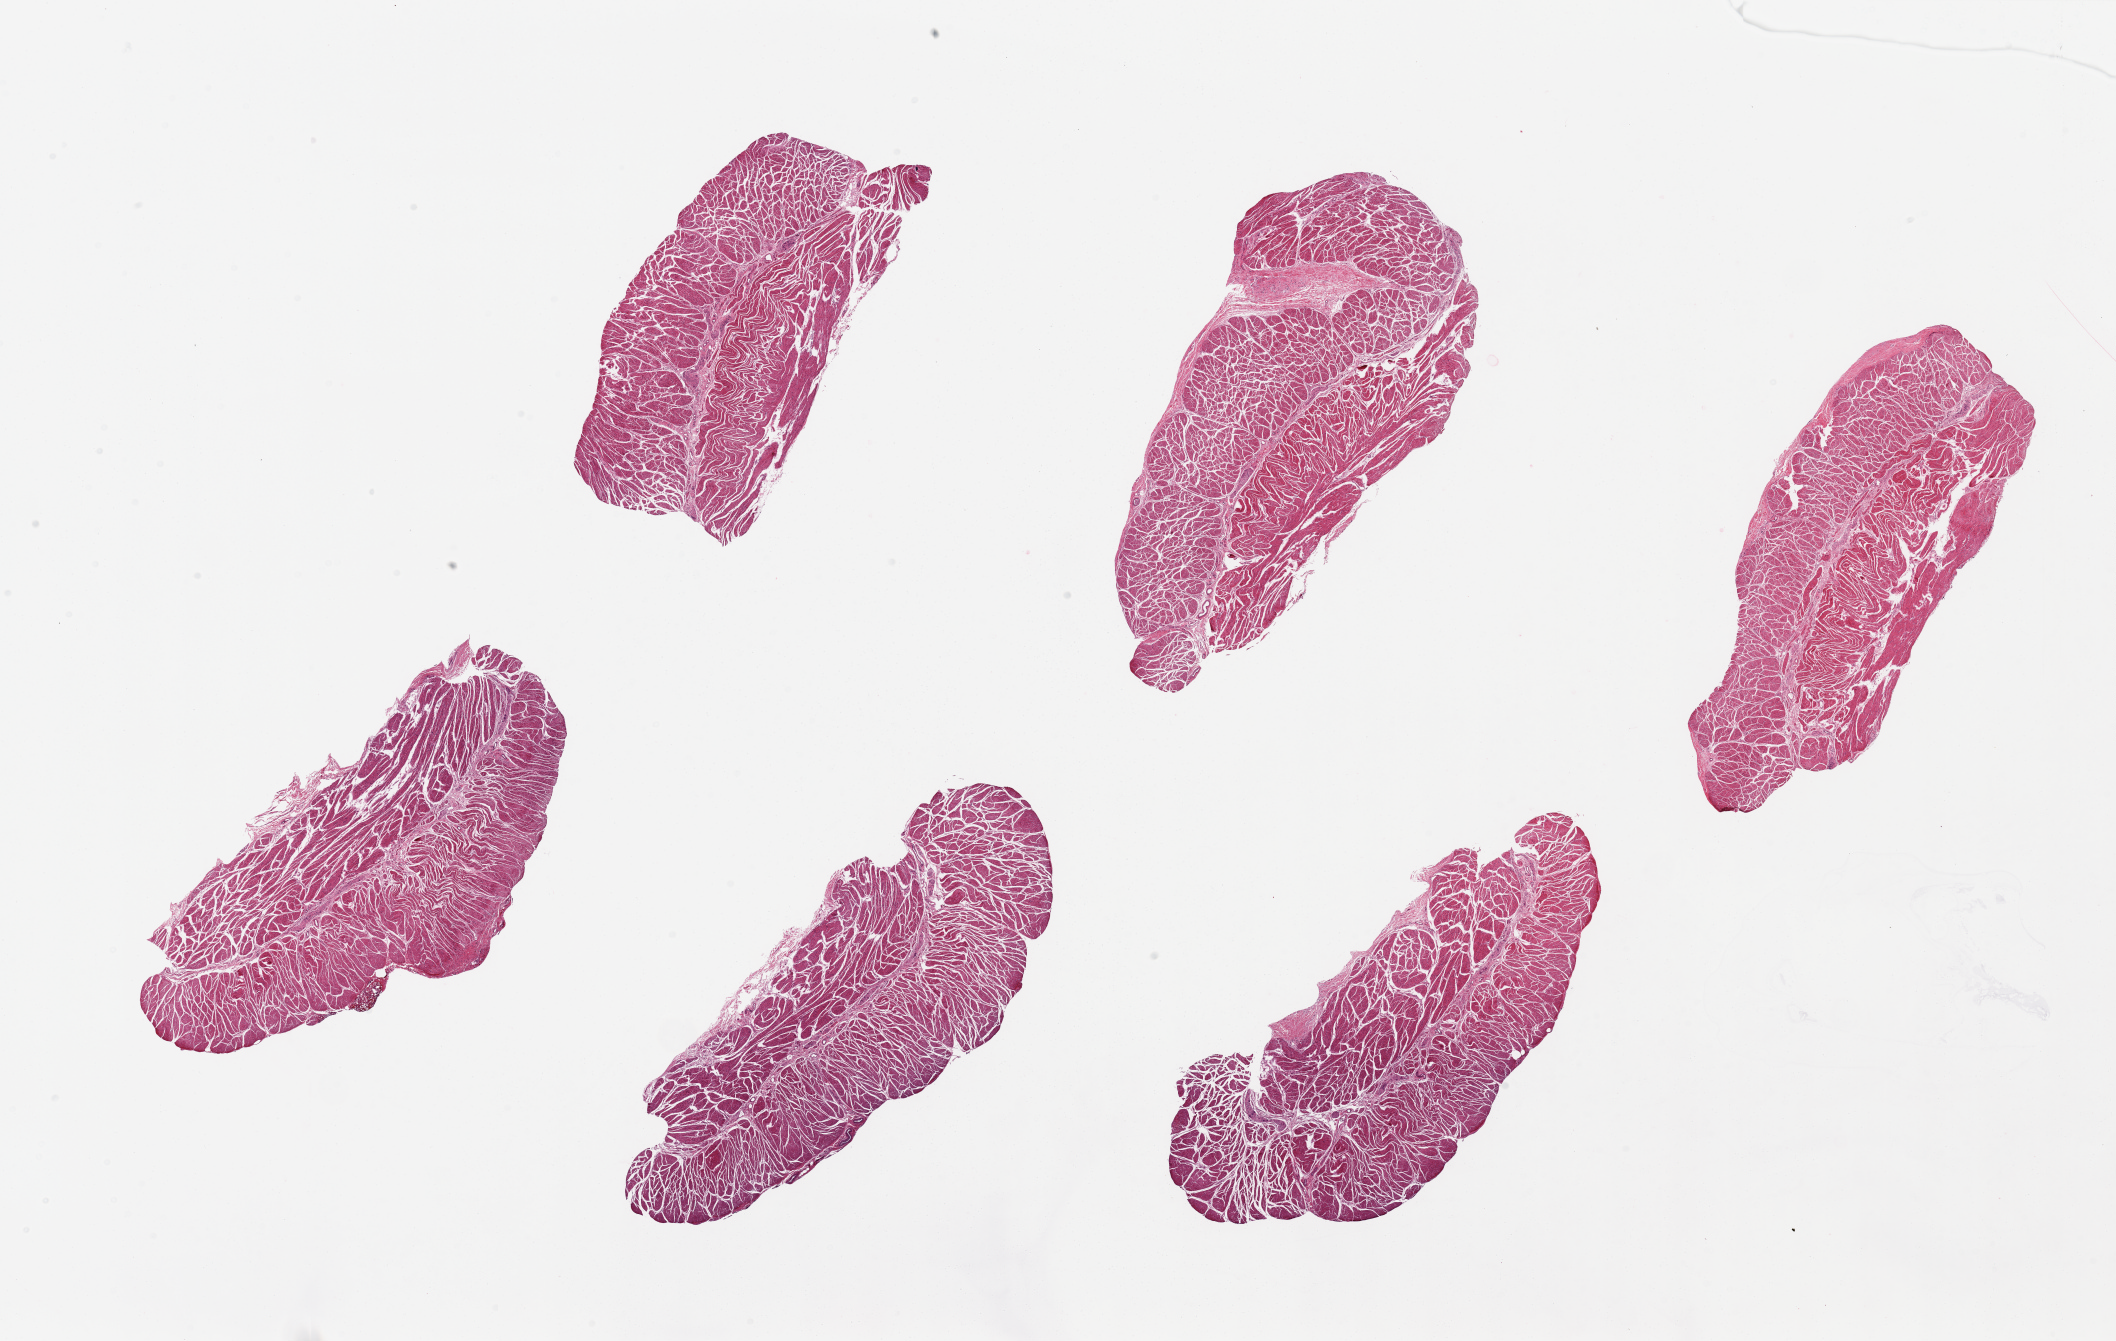
Whole-slide image, H&E stain, whole scanned area (about 33.5 x 21.2 mm) shown as a low-resolution overview. PAXgene-fixed, paraffin-embedded tissue. Target tissue: esophageal muscle. Donor tissue sample.
Reviewer comment on this tissue sample: 6 pieces, well-trimmed.